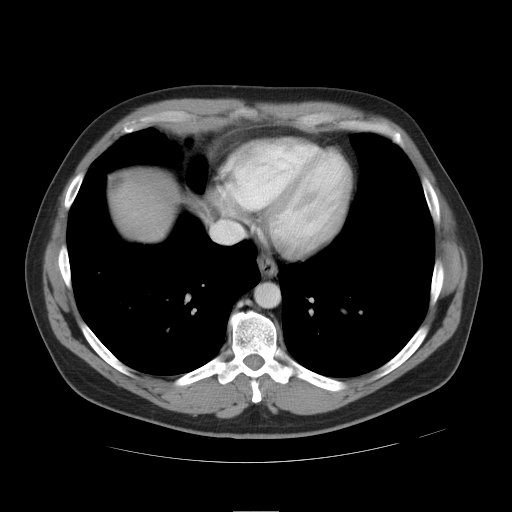
Contrast-enhanced abdominal CT, one axial slice. Slice 44 of 49 in the series (ordered by position). Reconstruction kernel STANDARD. 120 kVp. Soft-tissue window (W 400 / L 40 HU). 512 × 512 image matrix. Male patient, age 52 years. From the clinical record (not read from this slice): diagnosis: colorectal cancer liver metastases, imaged before liver resection; multiple liver metastases: yes; largest metastasis: 5.1 cm; disease in both lobes: yes.
Annotated regions visible in this slice (outlined manually by an expert reader):
- liver: bounding box (x1, y1, x2, y2) in pixels: (114, 182, 172, 238)